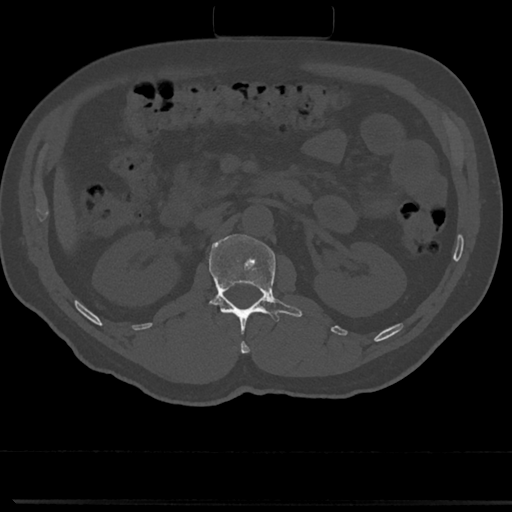
CT including the spine, one axial slice; slice 76 of 817 in the series (ordered by position); bone window (W 1800 / L 400 HU); 0.5 mm slice thickness; 512 × 512 image matrix, field of view 355 × 355 mm. Patient: male, 61 years. From the clinical record (not read from this slice): primary cancer: prostate.
Annotated regions visible in this slice (semi-automatic segmentation, software-assisted and operator-edited):
- L1 vertebra: bounding box [x1, y1, x2, y2] px = [191, 236, 301, 350]